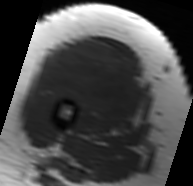
MRI of an extremity soft-tissue mass, one axial slice. Position 30 of 91 along the scan axis. MR volume resampled by the dataset authors to the PET/CT grid (not the native acquisition matrix). 3.27 mm slice thickness. 193 × 186 image matrix, field of view 188 × 182 mm. Female patient. Case-level facts recorded for this patient, not image findings: histological type: malignant solitary fibrous tumor; grade: intermediate; site of the primary tumour: right thigh.
Annotated regions visible in this slice (expert contour drawn on MRI and transferred to this co-registered scan by the dataset authors):
- gross tumour volume including surrounding oedema: bounding box [x1, y1, x2, y2] px = [40, 39, 148, 125]
- gross tumour volume (mass): [44, 39, 144, 120]